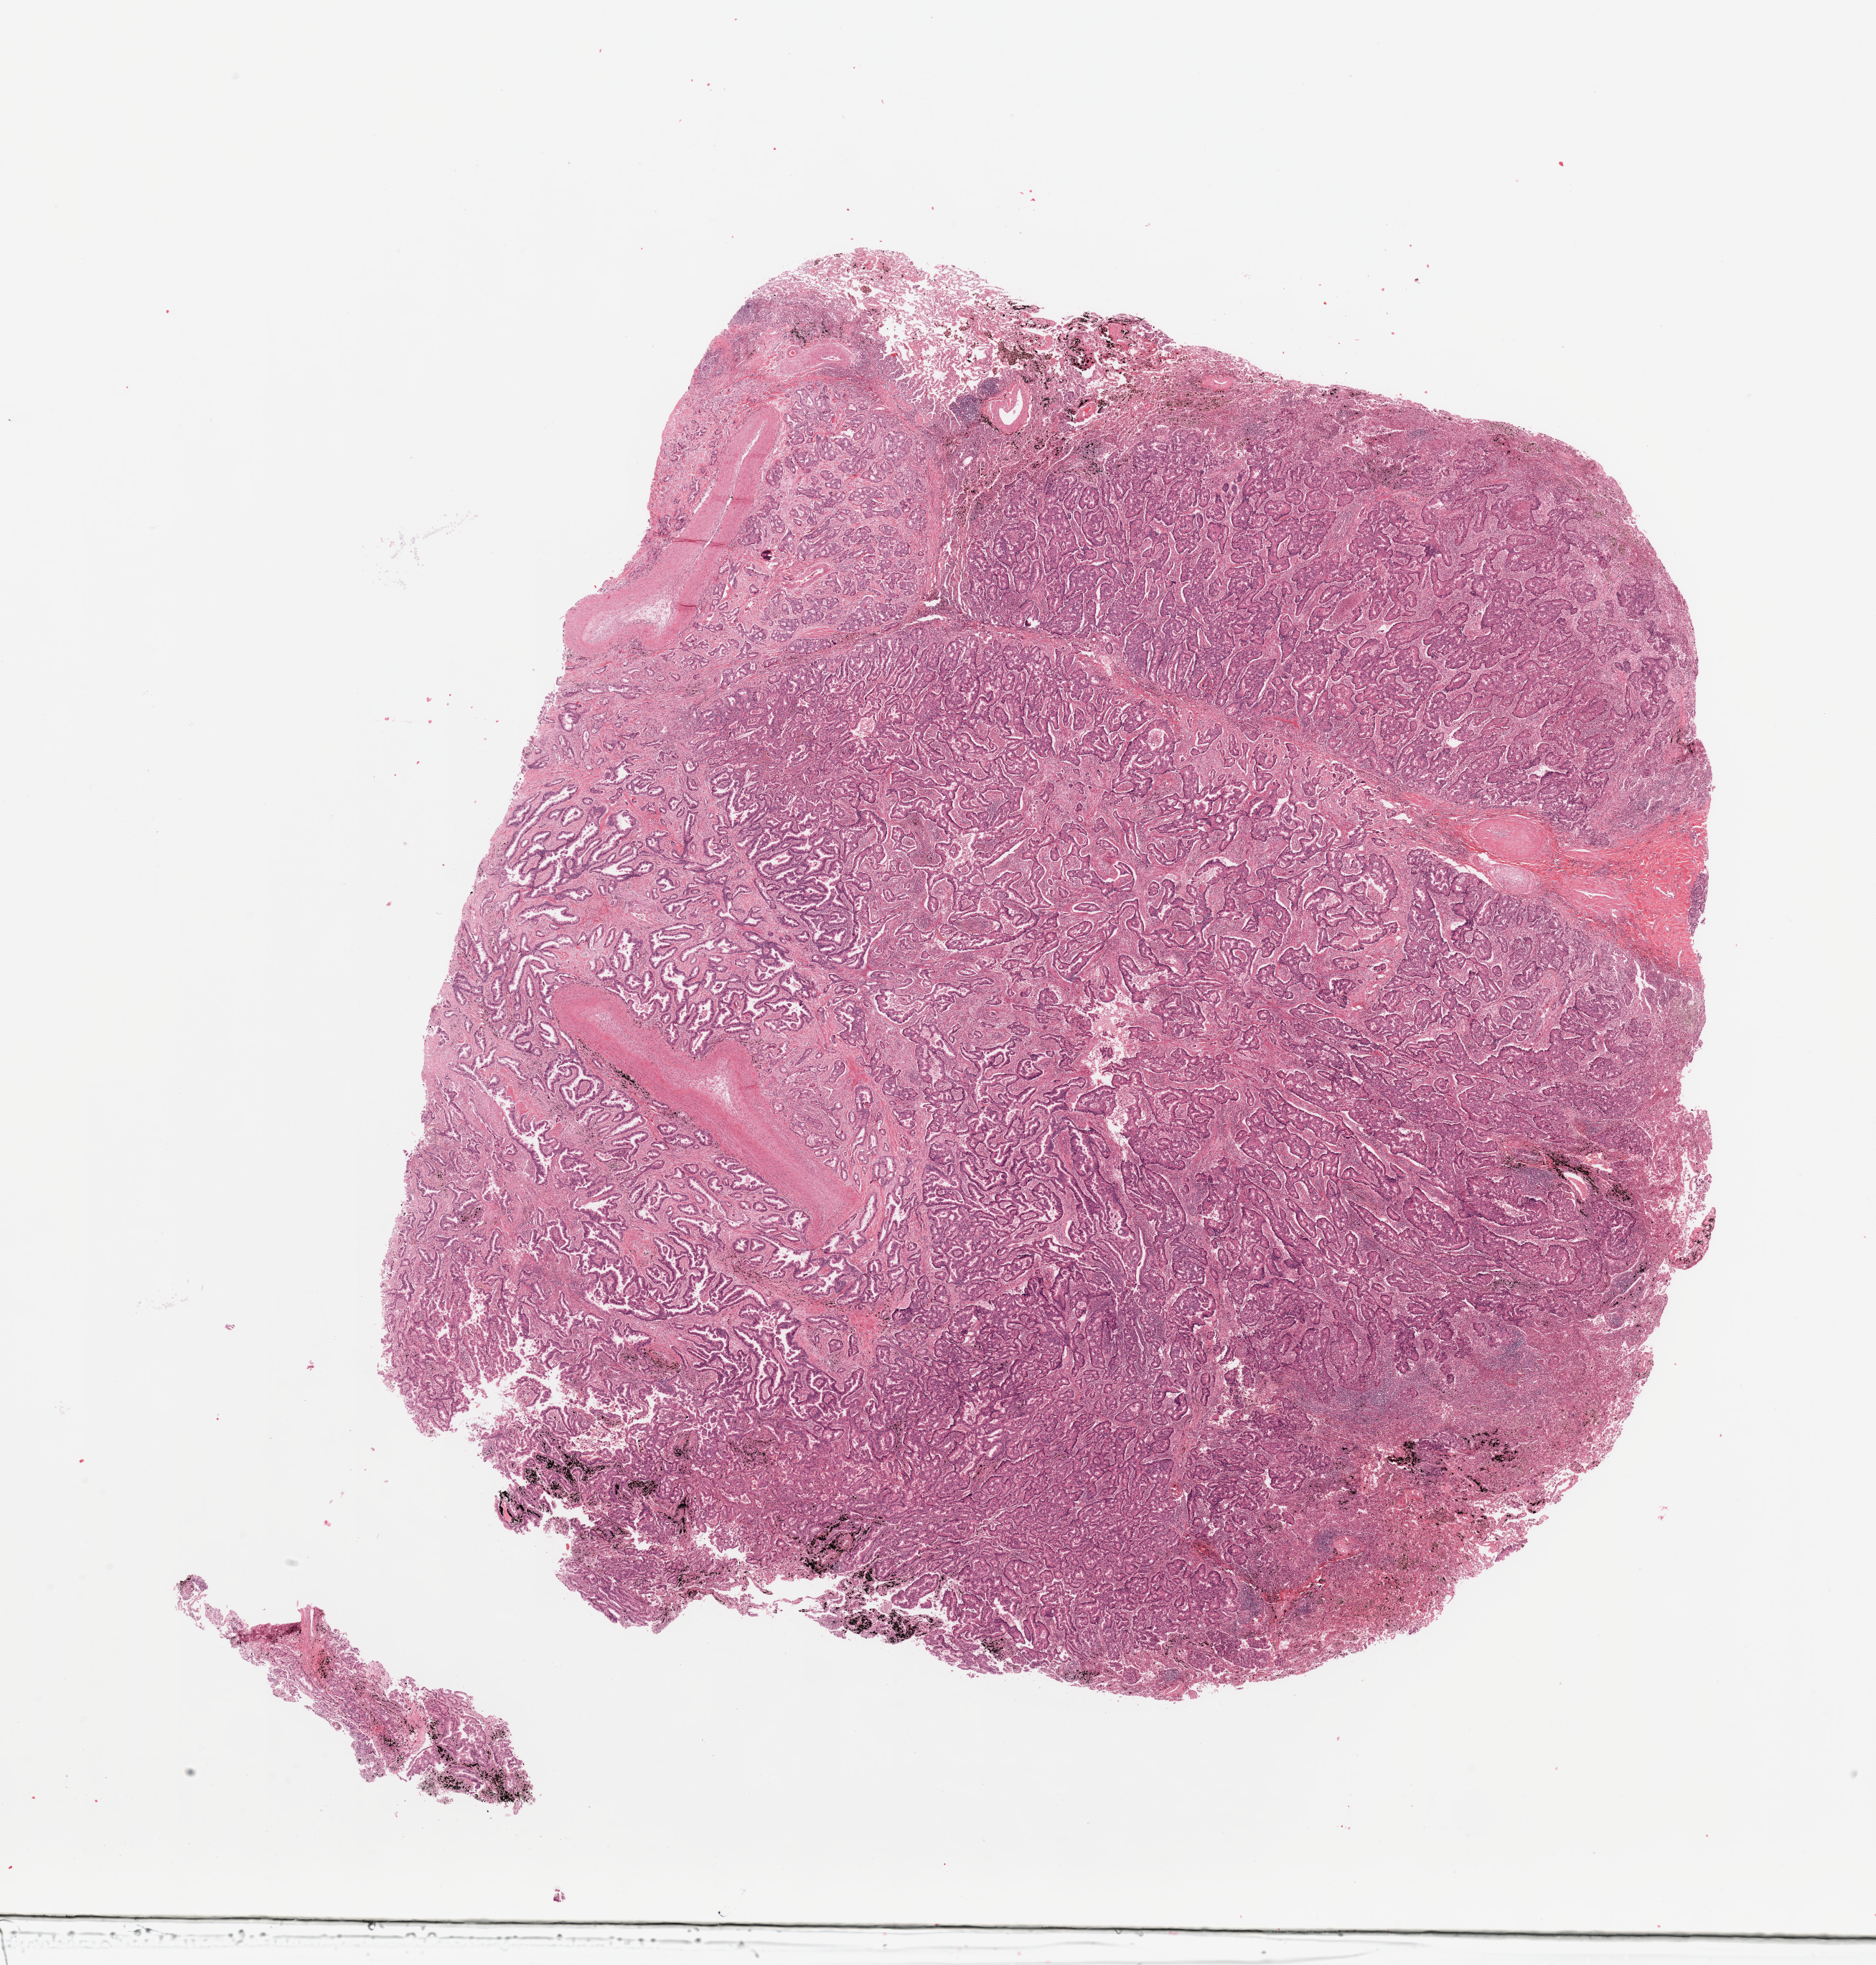
Digitized H&E-stained tissue section (whole slide) — whole scanned area (about 20.7 x 21.7 mm, slide scanned at 20x) shown as a low-resolution overview; lung, tumour tissue. Patient: male, age 60 years. Histologic grade: G2 (moderately differentiated).
Diagnosis: Adenocarcinoma, NOS. AJCC pathologic stage: IIA.